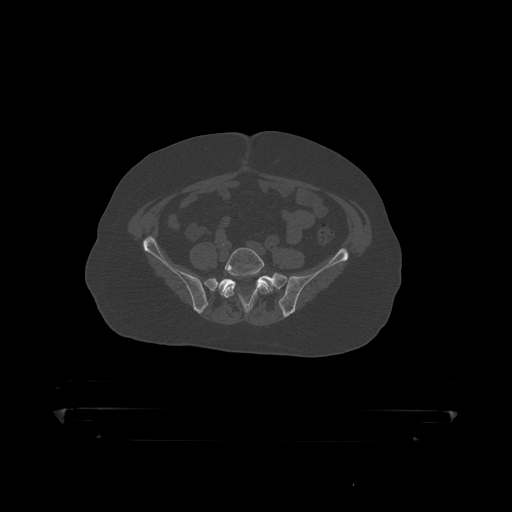
CT including the spine, one axial slice. Slice 31 of 390 in the series (ordered by position). Reconstruction kernel STANDARD. 120 kVp. Bone window (W 1800 / L 400 HU). 1.25 mm slice thickness. 512 × 512 image matrix. Male patient, age 60 years. Case-level facts recorded for this patient, not image findings: primary cancer: prostate.
Structures marked on this image (semi-automatically segmented with operator editing):
- L5 vertebra: box from (x=224, y=248) to (x=270, y=307) px